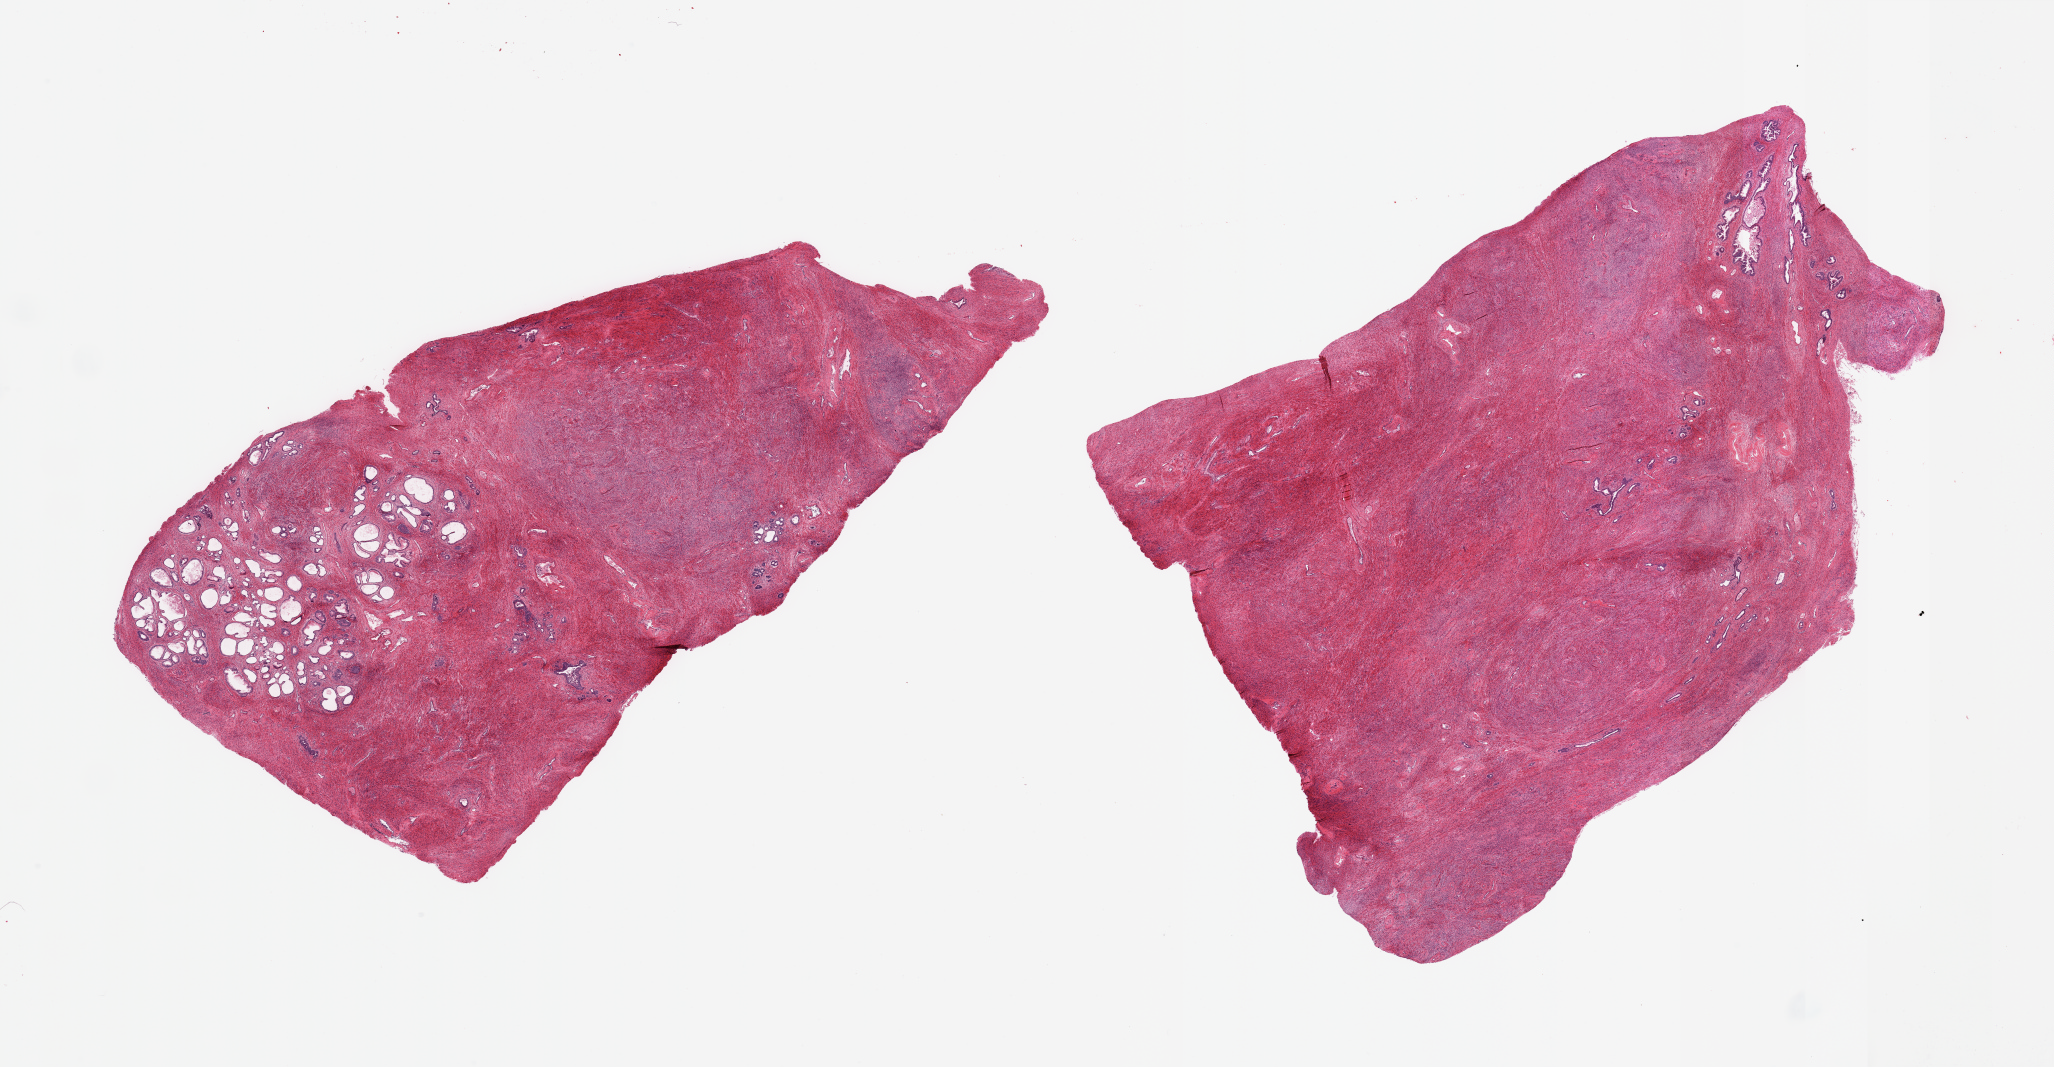
Whole-slide image, hematoxylin and eosin (H&E) stain, shown as a low-resolution overview of the whole scanned area (about 32.5 x 16.9 mm, acquisition: 20x scan); PAXgene-fixed, paraffin-embedded tissue; sampled site (target tissue): prostate; tissue donor sample. Donor sex: male.
Reviewer comment on this tissue sample: 2 pieces; stromal hyperplasia with residual glandular component and focal glandular hyperplasia.